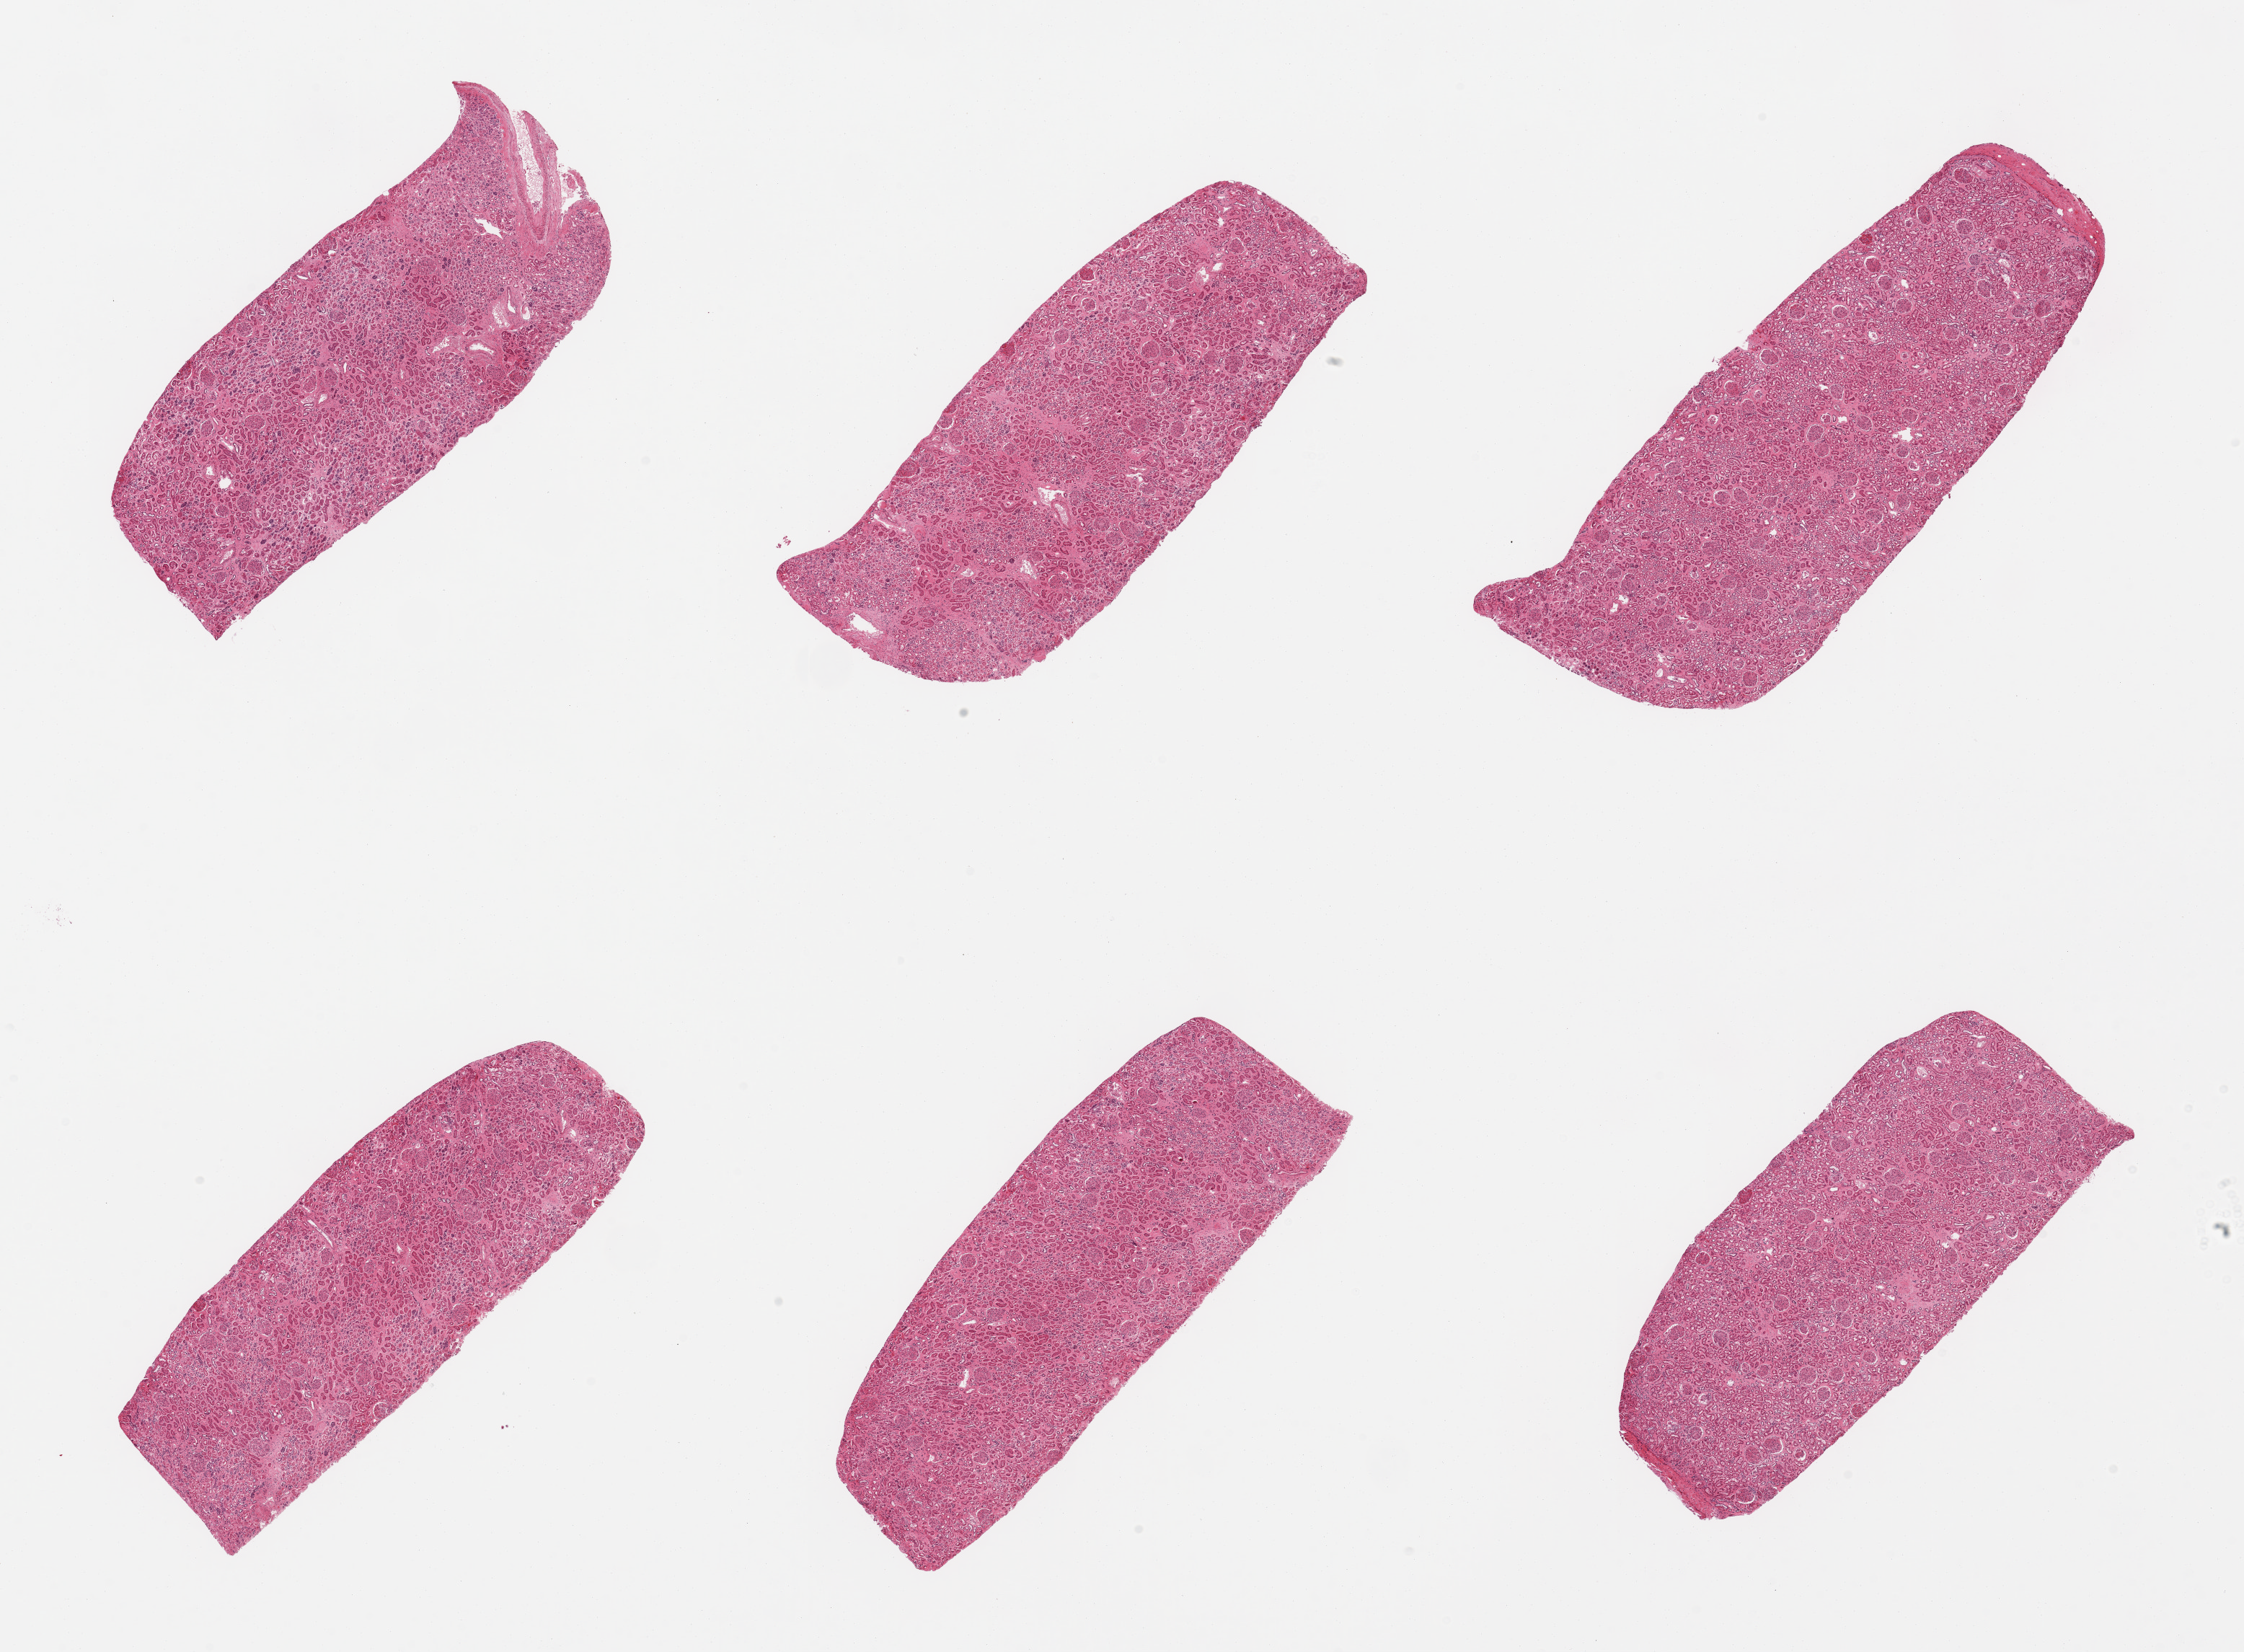
Whole-slide image, hematoxylin and eosin (H&E) stain — whole scanned area (about 24.6 x 18.1 mm) shown as a low-resolution overview; PAXgene-fixed, paraffin-embedded tissue; sampled site (target tissue): renal cortex; donor tissue sample. Donor sex: male.
Review note (as recorded): 6 pieces; mild diffuse interstitial fibrosis.